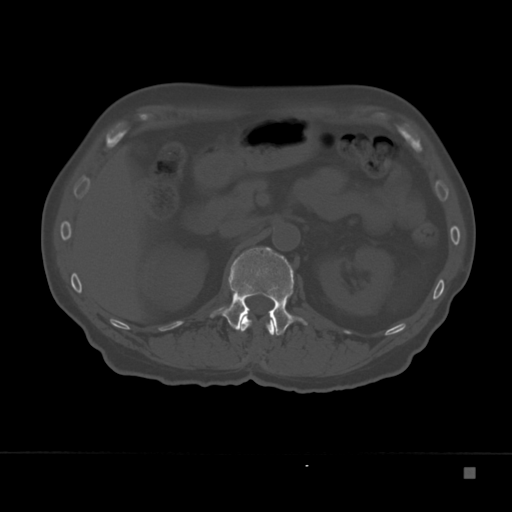
CT including the spine, one axial slice; slice 116 of 332 in the series (ordered by position); reconstruction kernel Br40s; bone window (W 1800 / L 400 HU); 512 × 512 image matrix, field of view 389 × 389 mm. Patient: male, 72 years. From the clinical record (not read from this slice): primary cancer: skeletal.
Outlined on this slice (semi-automatic segmentation, software-assisted and operator-edited):
- L1 vertebra: bounding box [x1, y1, x2, y2] px = [210, 247, 308, 336]
- T12 vertebra: [241, 317, 274, 335]